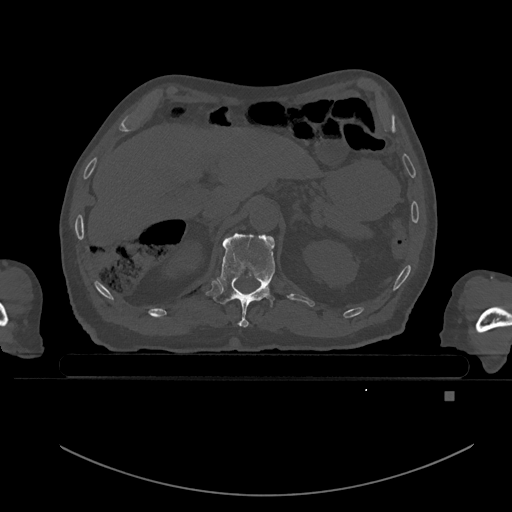
CT including the spine, one axial slice. Position 26 of 969 along the scan axis. Bone window (W 1800 / L 400 HU). 0.5 mm slice thickness. 512 × 512 image matrix, field of view 456 × 456 mm. Patient: male, 82 years. Case-level facts recorded for this patient, not image findings: primary cancer: prostate; vertebrae with lytic lesions (as recorded): T11, T9, T8, T2.
Annotated regions visible in this slice (semi-automatic segmentation, software-assisted and operator-edited):
- T11 vertebra: bounding box <214,233,275,327> (left, top, right, bottom; pixels)